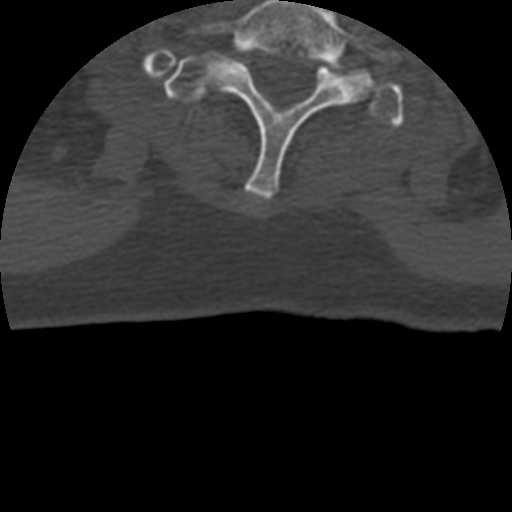
CT including the spine, one axial slice. Slice 392 of 399 in the series (ordered by position). Reconstruction kernel STANDARD. Bone window (W 1800 / L 400 HU). 512 × 512 image matrix, field of view 160 × 160 mm. Patient age 69 years. Case-level facts recorded for this patient, not image findings: primary cancer: prostate.
Structures marked on this image (semi-automatic segmentation, software-assisted and operator-edited):
- T1 vertebra: box from (x=163, y=52) to (x=406, y=129) px